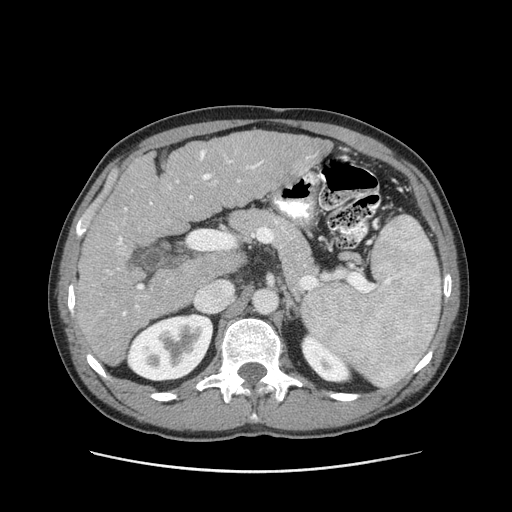
Contrast-enhanced abdominal CT (liver protocol), one axial slice; reconstruction kernel STANDARD; 120 kVp; soft-tissue window (W 400 / L 40 HU); 2.5 mm slice thickness; 512 × 512 image matrix, field of view 380 × 380 mm. Case-level facts recorded for this patient, not image findings: diagnosis: hepatocellular carcinoma (patient treated with transarterial chemoembolisation; whether this scan precedes or follows treatment is not stated here); TNM stage (as recorded): Stage-II; Child-Pugh class: A; tumour differentiation: moderately differentiated; tumour nodularity: multinodular.
Outlined on this slice (semi-automatic segmentation, software-assisted and operator-edited):
- liver parenchyma outside the tumour (the mass and vessels are separate outlines, so this box may not span the whole liver): bounding box (x1, y1, x2, y2) in pixels: (74, 130, 330, 366)
- liver vessels: (107, 150, 263, 316)